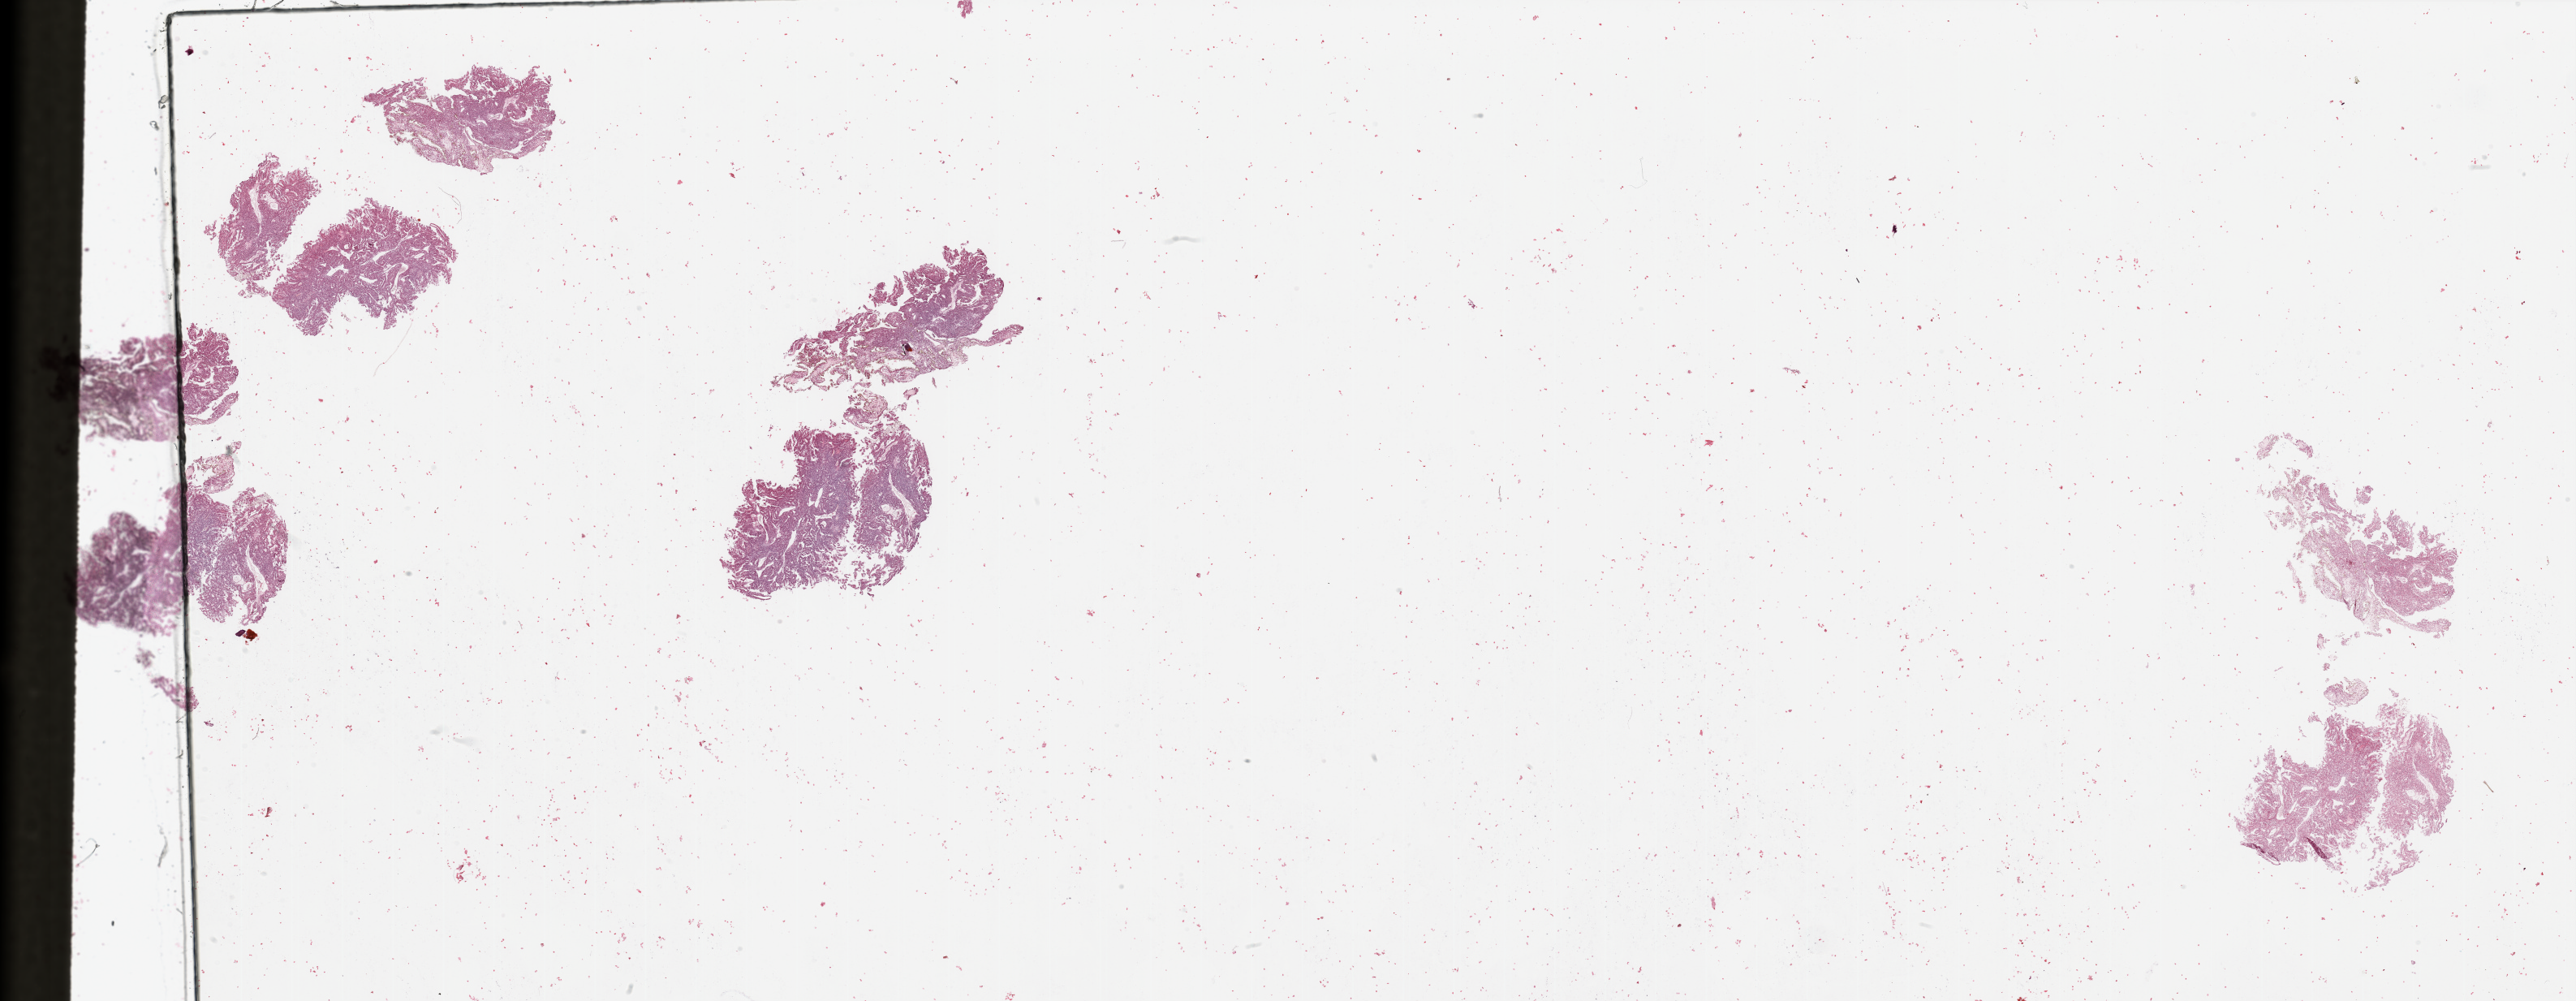
Digitized H&E tissue section (whole slide), whole scanned area (about 50.2 x 19.5 mm, slide scanned at 20x) shown as a low-resolution overview; tumour tissue sample, sampled site: kidney. 65-year-old male patient. Histologic grade: G2 (moderately differentiated). Pathologist review of this section (percent, as recorded): tumour nuclei 90%, necrosis 0%.
- primary tumour site (as recorded): upper pole
- AJCC pathologic stage: I
- diagnosis: Renal cell carcinoma, NOS